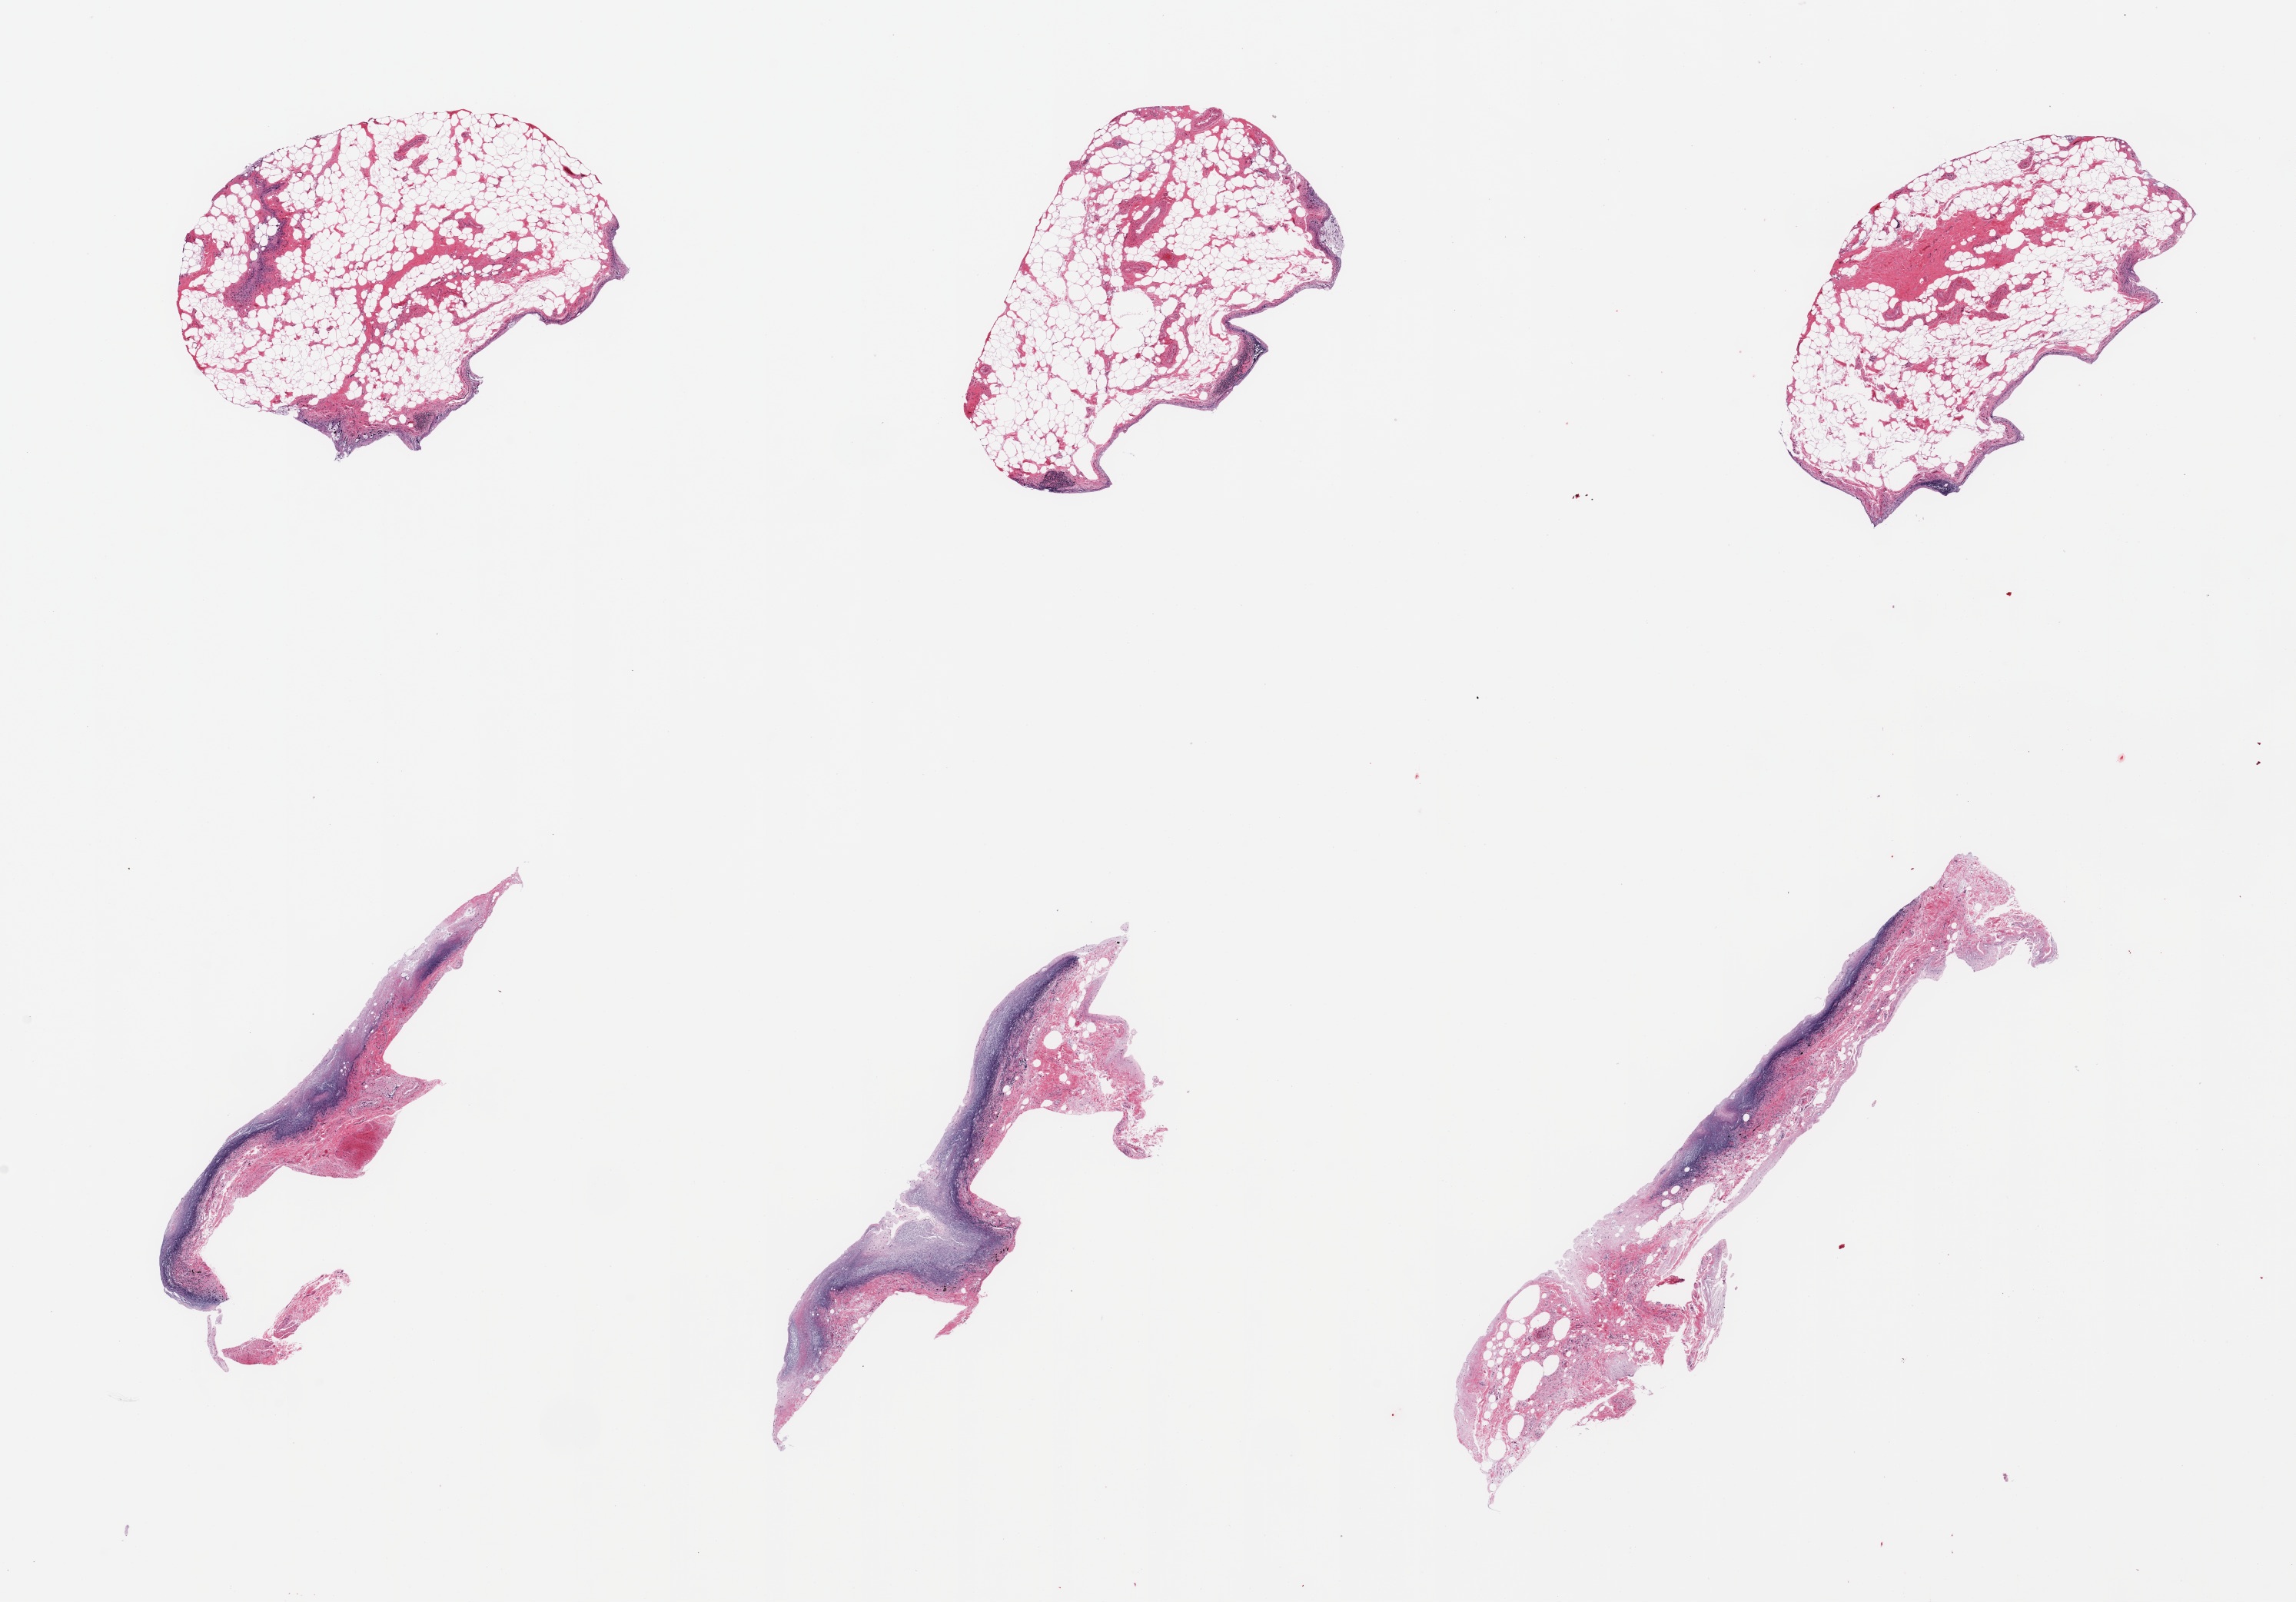
Whole-slide image, haematoxylin and eosin stain, brightfield — a low-resolution overview of the entire scanned area, about 23.6 x 16.5 mm; PAXgene-fixed, paraffin-embedded tissue; target tissue: ileum; tissue donor sample. Donor: male.
Pathologist's review note for this sample: 6 pieces, ~50% fat, <5% target lymphoid aggregates.